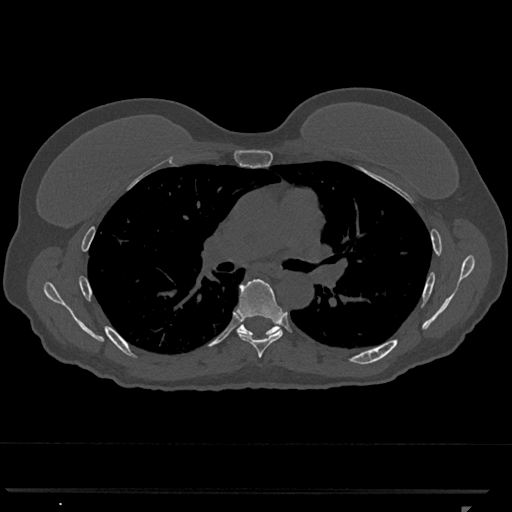
CT including the spine, one axial slice. Position 747 of 793 along the scan axis. Bone window (W 1800 / L 400 HU). 0.5 mm slice thickness. 512 × 512 image matrix, field of view 380 × 380 mm. Female patient, age 62 years. Case-level facts recorded for this patient, not image findings: primary cancer: renal.
Outlined on this slice (semi-automatic segmentation, software-assisted and operator-edited):
- T6 vertebra: bounding box [x1, y1, x2, y2] px = [237, 279, 284, 358]
- T7 vertebra: [237, 324, 279, 337]